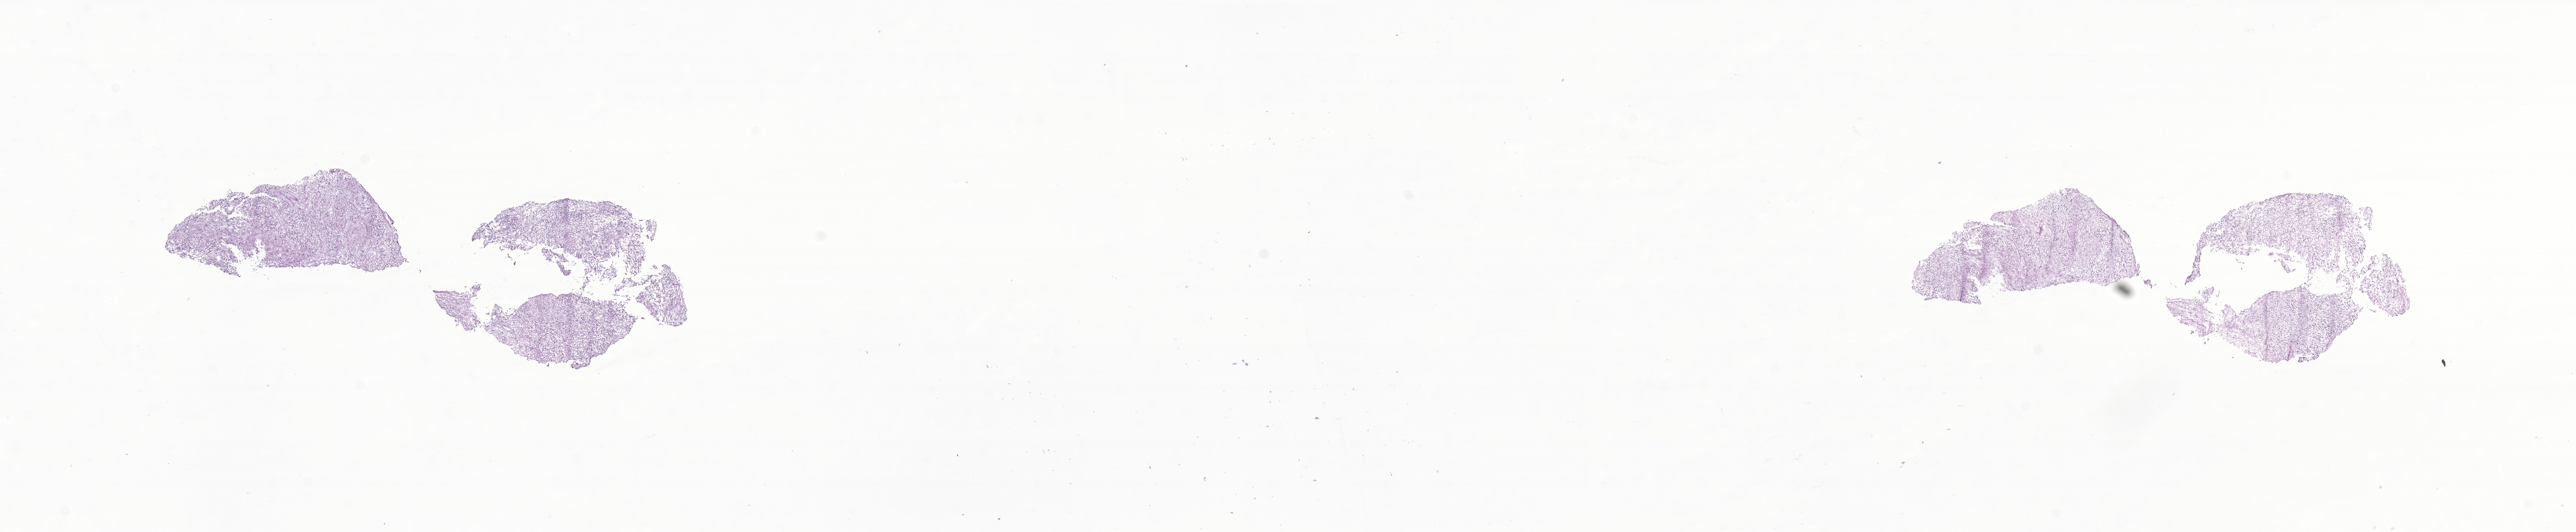
Digitized H&E-stained section of tumor tissue from the brain — low-resolution overview of the scanned area, about 28.6 x 5.9 mm, frozen section. Male patient, age 126 months.
Diagnosis: Ependymoma, NOS.